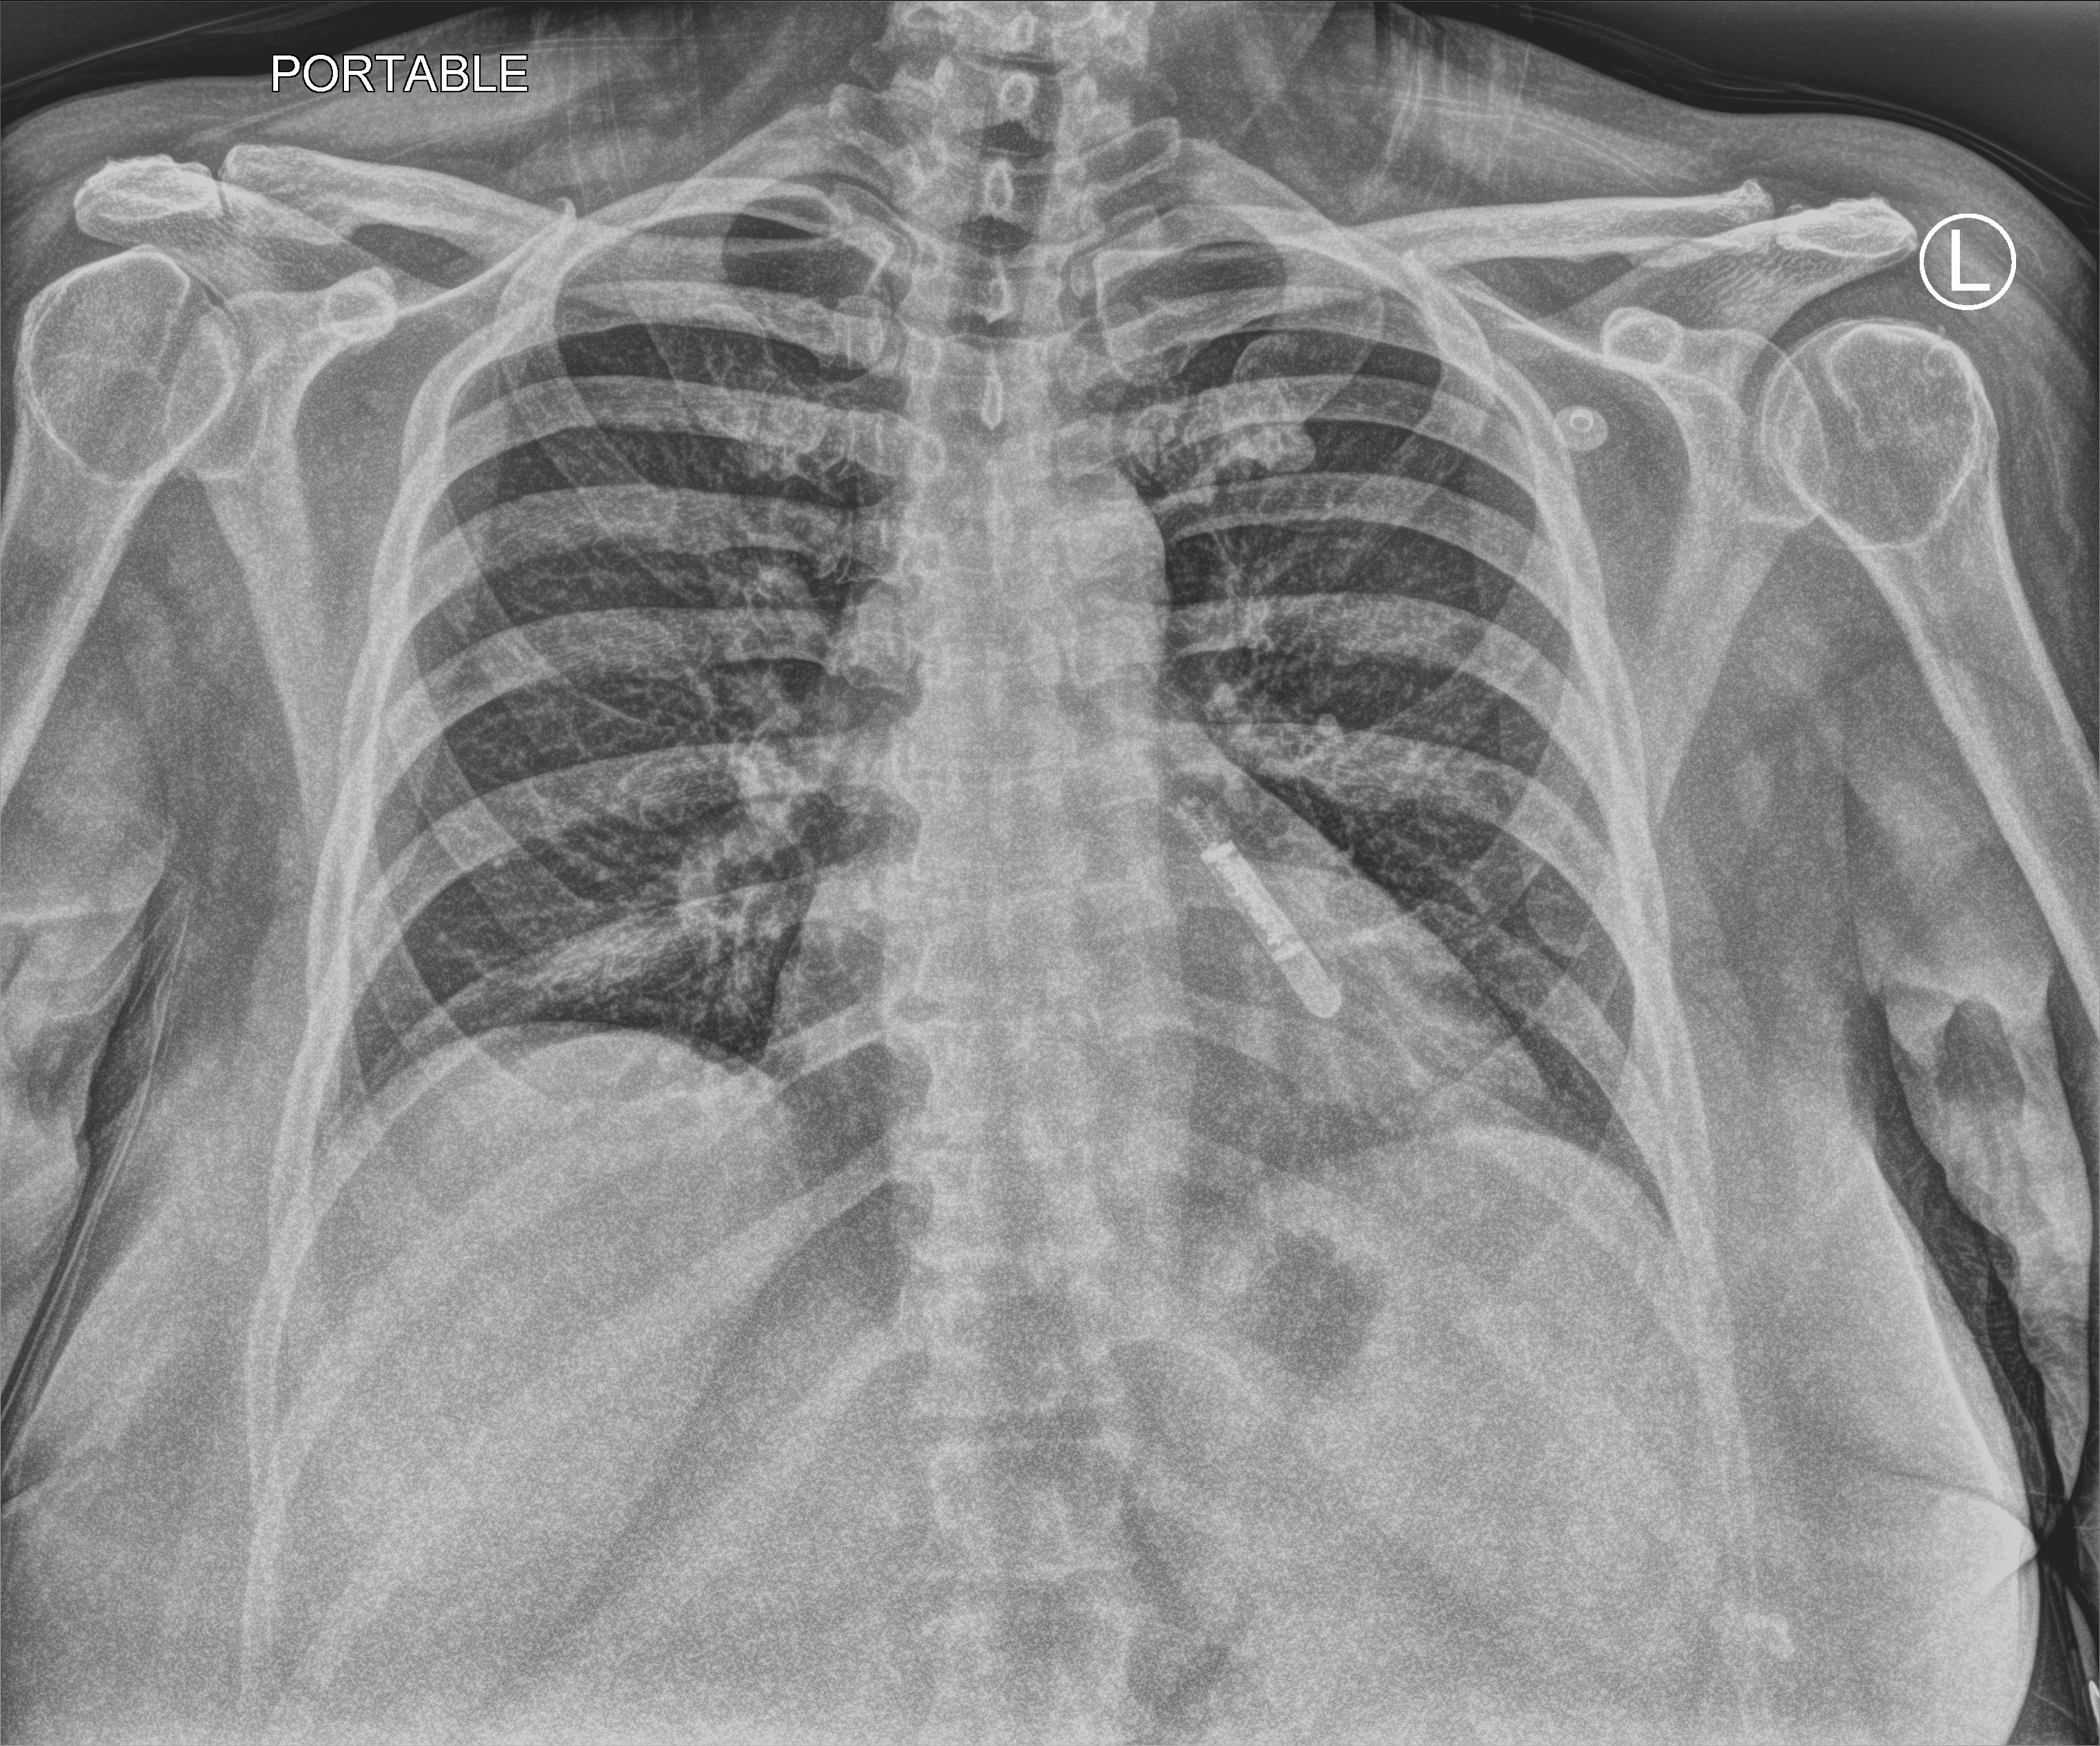
Chest X-ray (portable); anteroposterior (AP) projection. Patient hospitalised with COVID-19; female, aged 18–59 years.
From the hospital-stay record, not from the radiograph (when in the stay this image was taken is not recorded): chronic kidney disease (admission record): no.